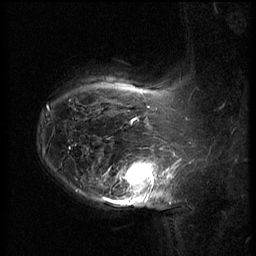
Breast MRI (dynamic contrast-enhanced), one sagittal slice; slice 49 of 62 in the series (ordered by position); 3 images stored at this slice position (order not interpretable as contrast timing); 1.5 T; TE 4.2 ms, TR 8.9 ms; 2.5 mm slice thickness; 256 × 256 image matrix, field of view 200 × 200 mm. Female patient, age 37 years. From the clinical record (not read from this slice): setting: breast cancer imaged before/during neoadjuvant chemotherapy; receptor status: triple-negative.
Outlined on this slice (semi-automatically segmented with operator editing):
- analysis volume of interest (the breast-tissue region the enhancement analysis was run in; not a lesion): bounding box (x1, y1, x2, y2) in pixels: (116, 146, 168, 203)
- tumour enhancement mask (voxels above the 140 % enhancement threshold inside the analysis volume of interest): (123, 163, 168, 202)